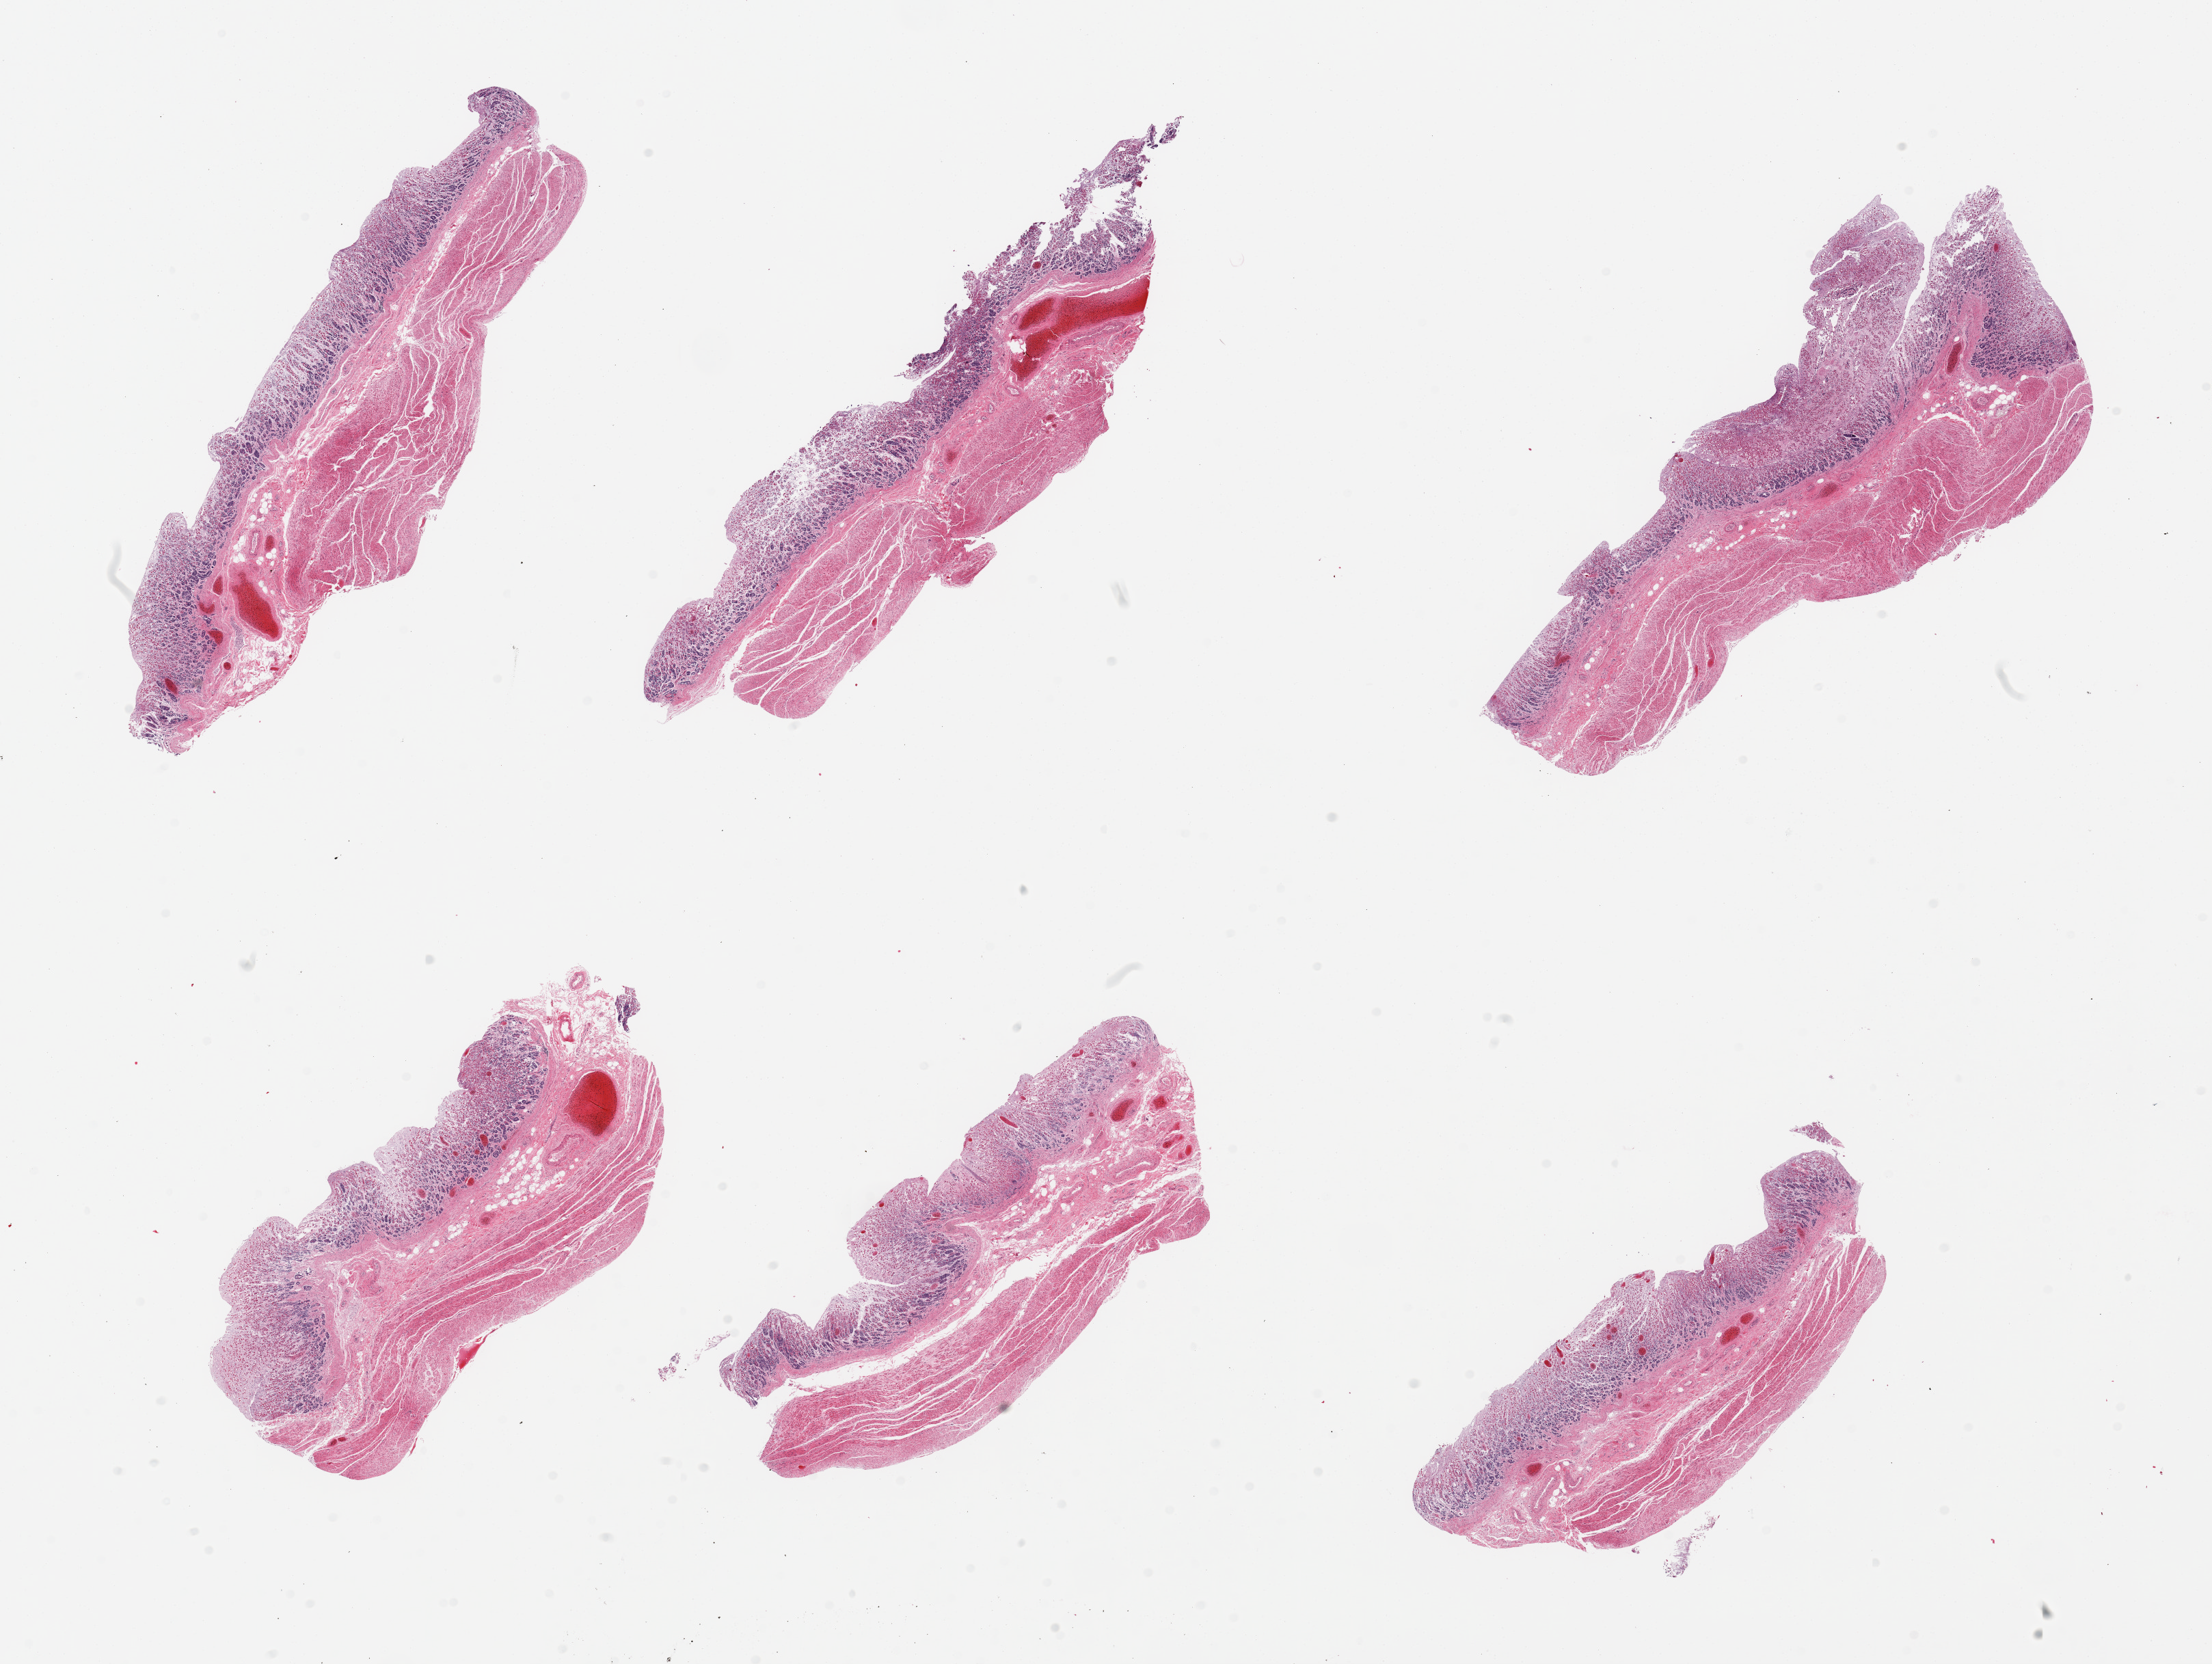
Digitized hematoxylin and eosin (H&E)-stained section, brightfield, whole scanned area (about 25.6 x 19.3 mm, from a 20x scan) shown as a low-resolution overview, PAXgene-fixed paraffin-embedded (PFPE) section, target tissue: stomach, donor tissue sample. Female donor.
- pathologist's review note for this sample: 6 pieces; mucosa largely autolyzed, muscularis moderately autolyzed